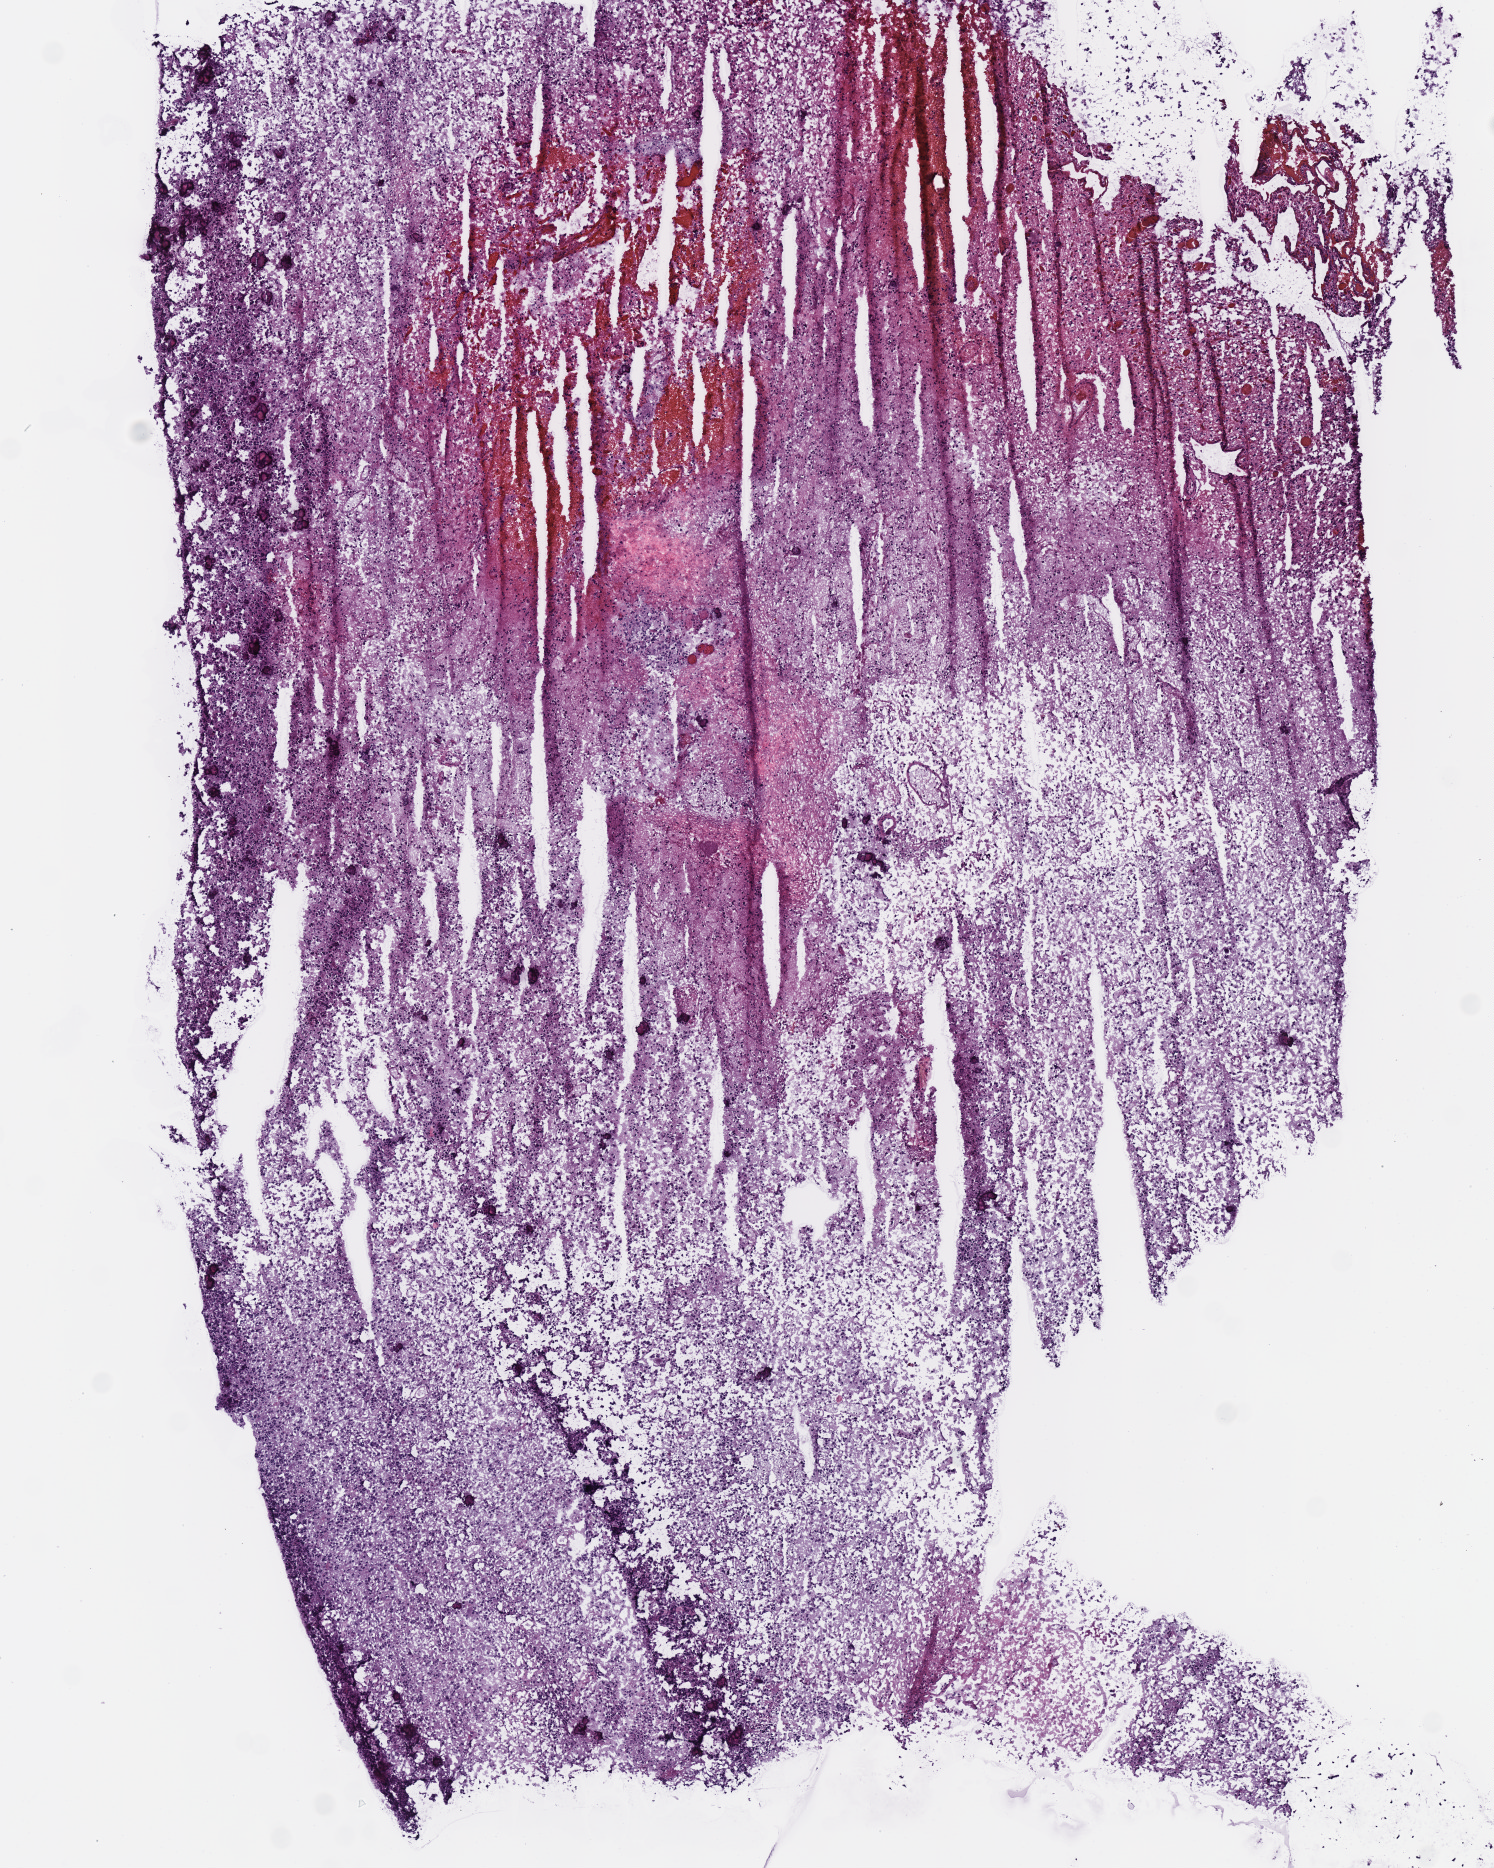
H&E-stained whole-slide image, low-resolution overview of the scanned area, about 5.9 x 7.3 mm. Frozen section from the top of the tissue portion. Brain, primary tumour sample. Patient: male, age at initial diagnosis 54 years. Histologic grade: G3 (poorly differentiated). Pathologist review of this section (percent, as recorded): tumour cells 100%, tumour nuclei 75%, normal cells 0%, stromal cells 0%, necrosis 0%.
Pathologic diagnosis: Oligodendroglioma, anaplastic (cerebrum). Laterality: right.